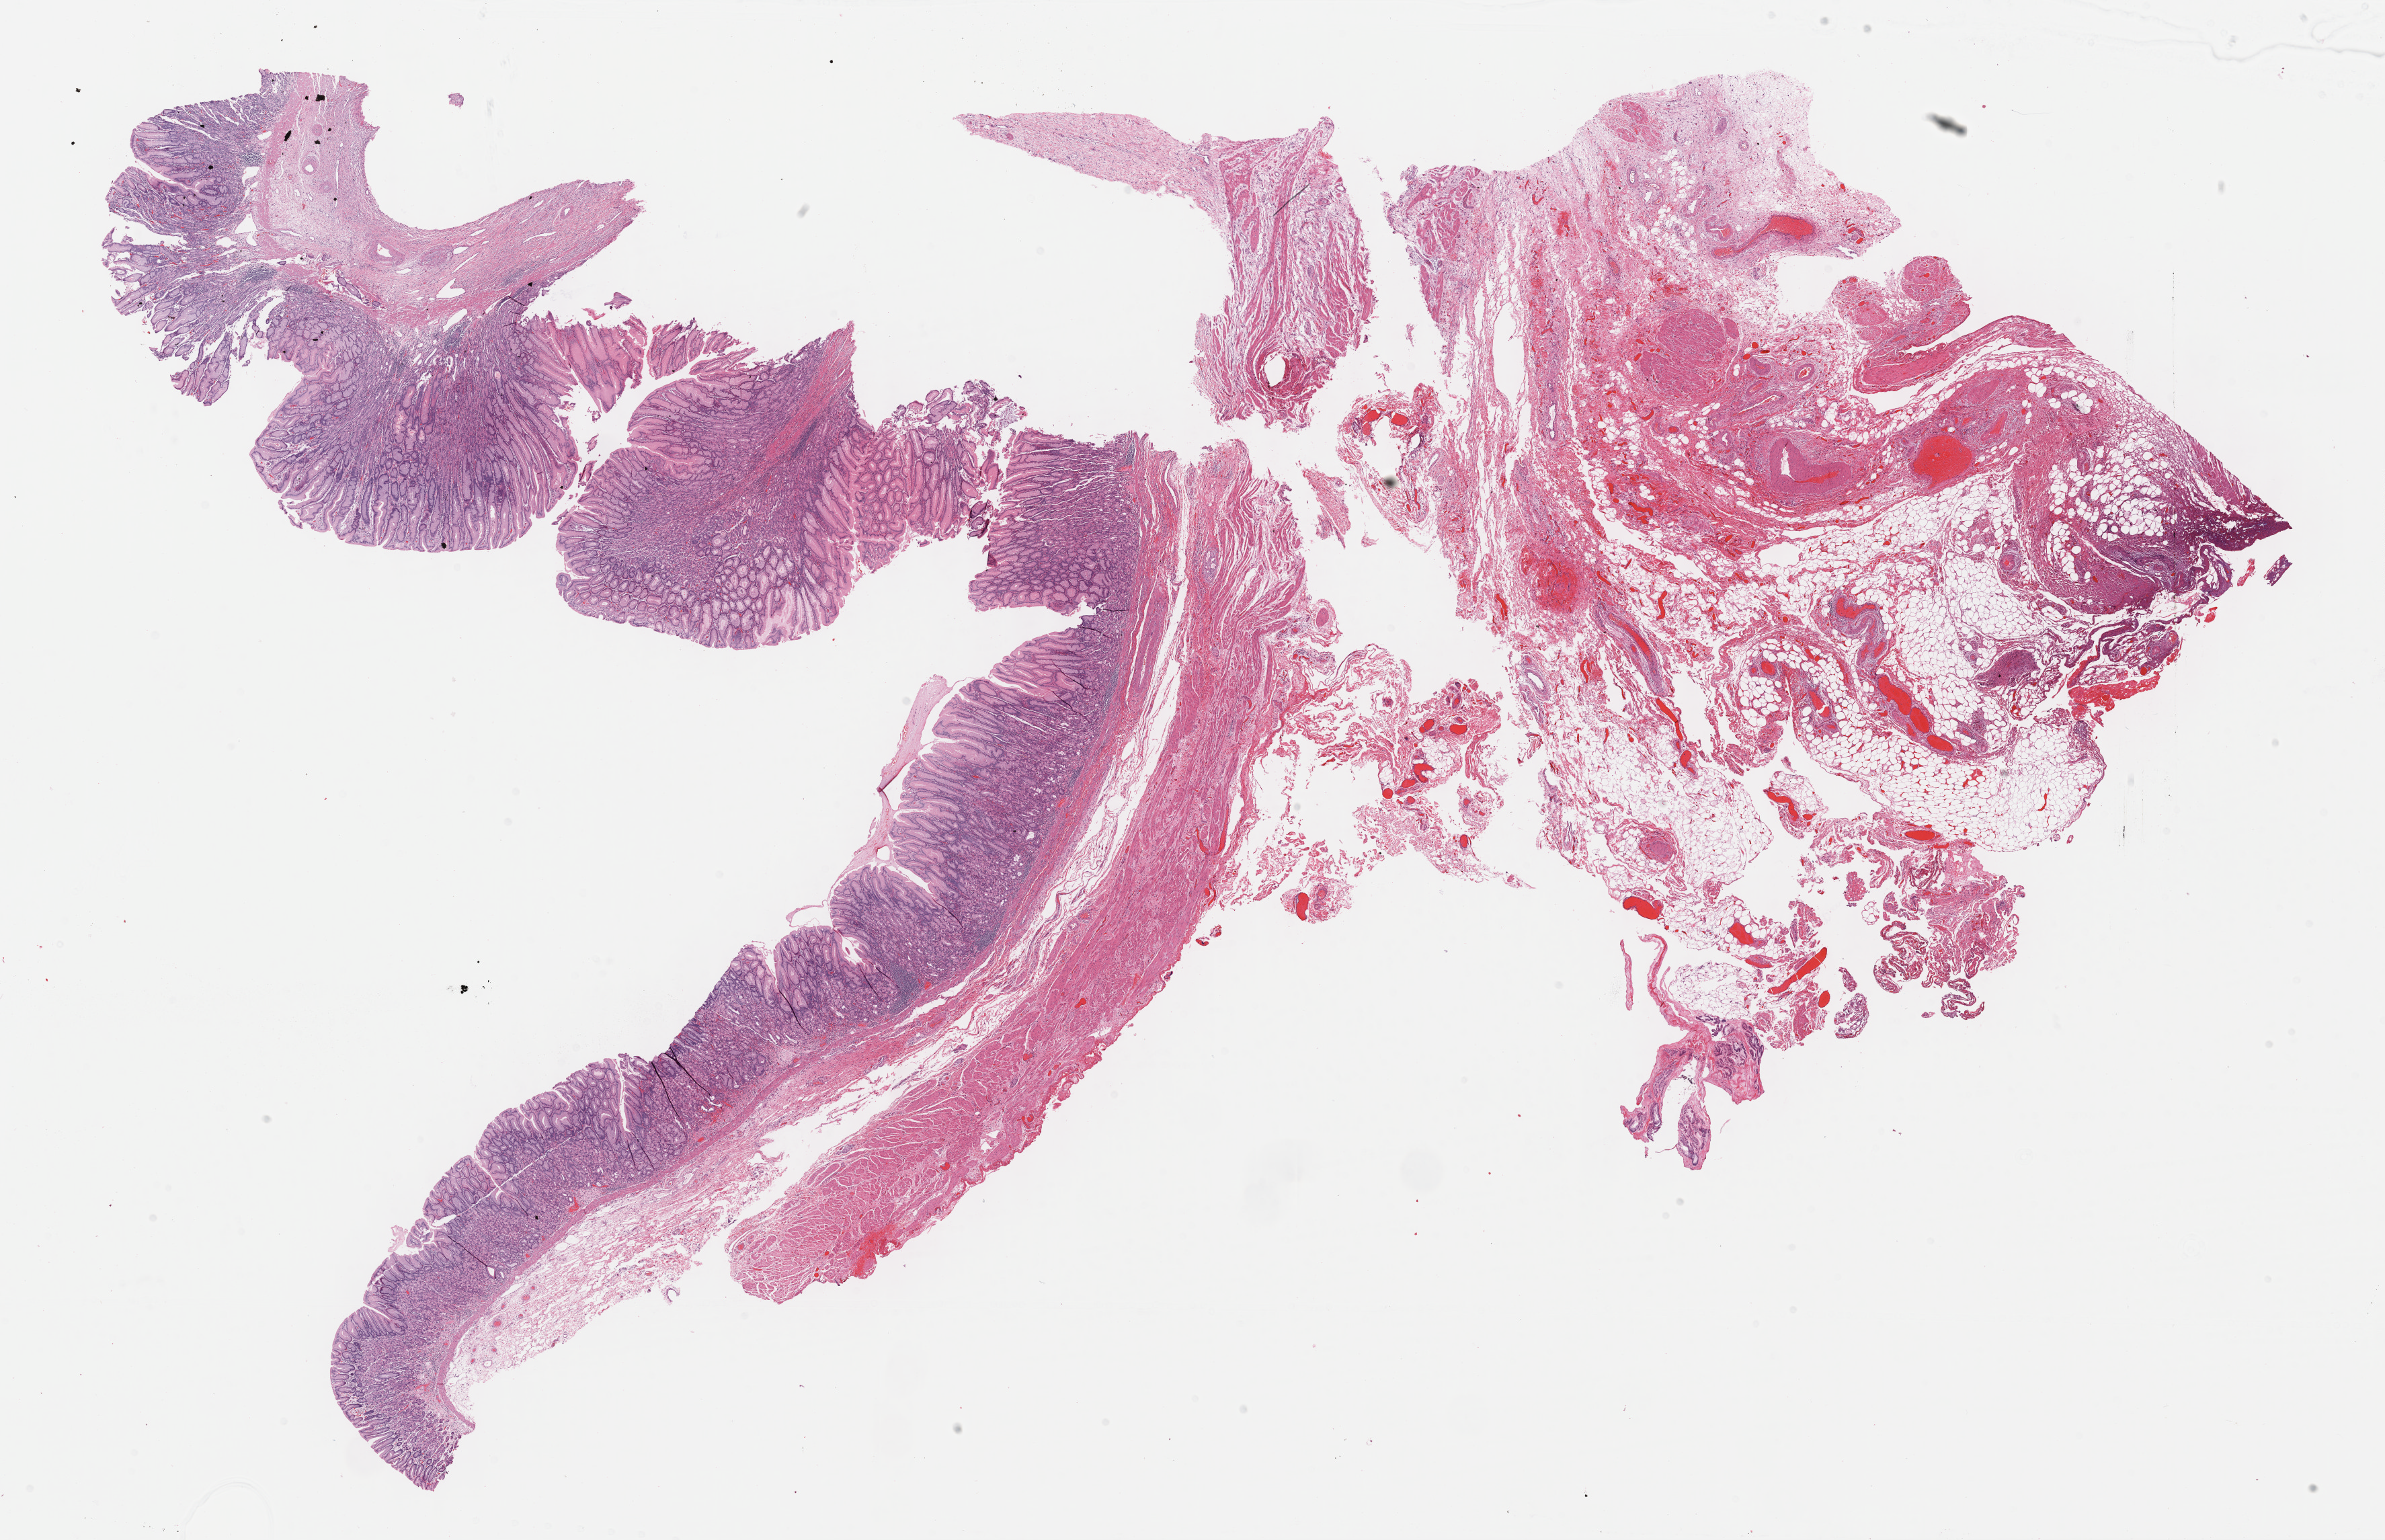
Digitized H&E-stained tissue section (whole slide), whole scanned area (about 28.7 x 18.5 mm, acquisition: 40x scan) shown as a low-resolution overview. Formalin-fixed paraffin-embedded (FFPE) diagnostic section. Primary tumour sample from the stomach. Patient: female, age at initial diagnosis 58 years.
Histologic diagnosis: Leiomyosarcoma, NOS.